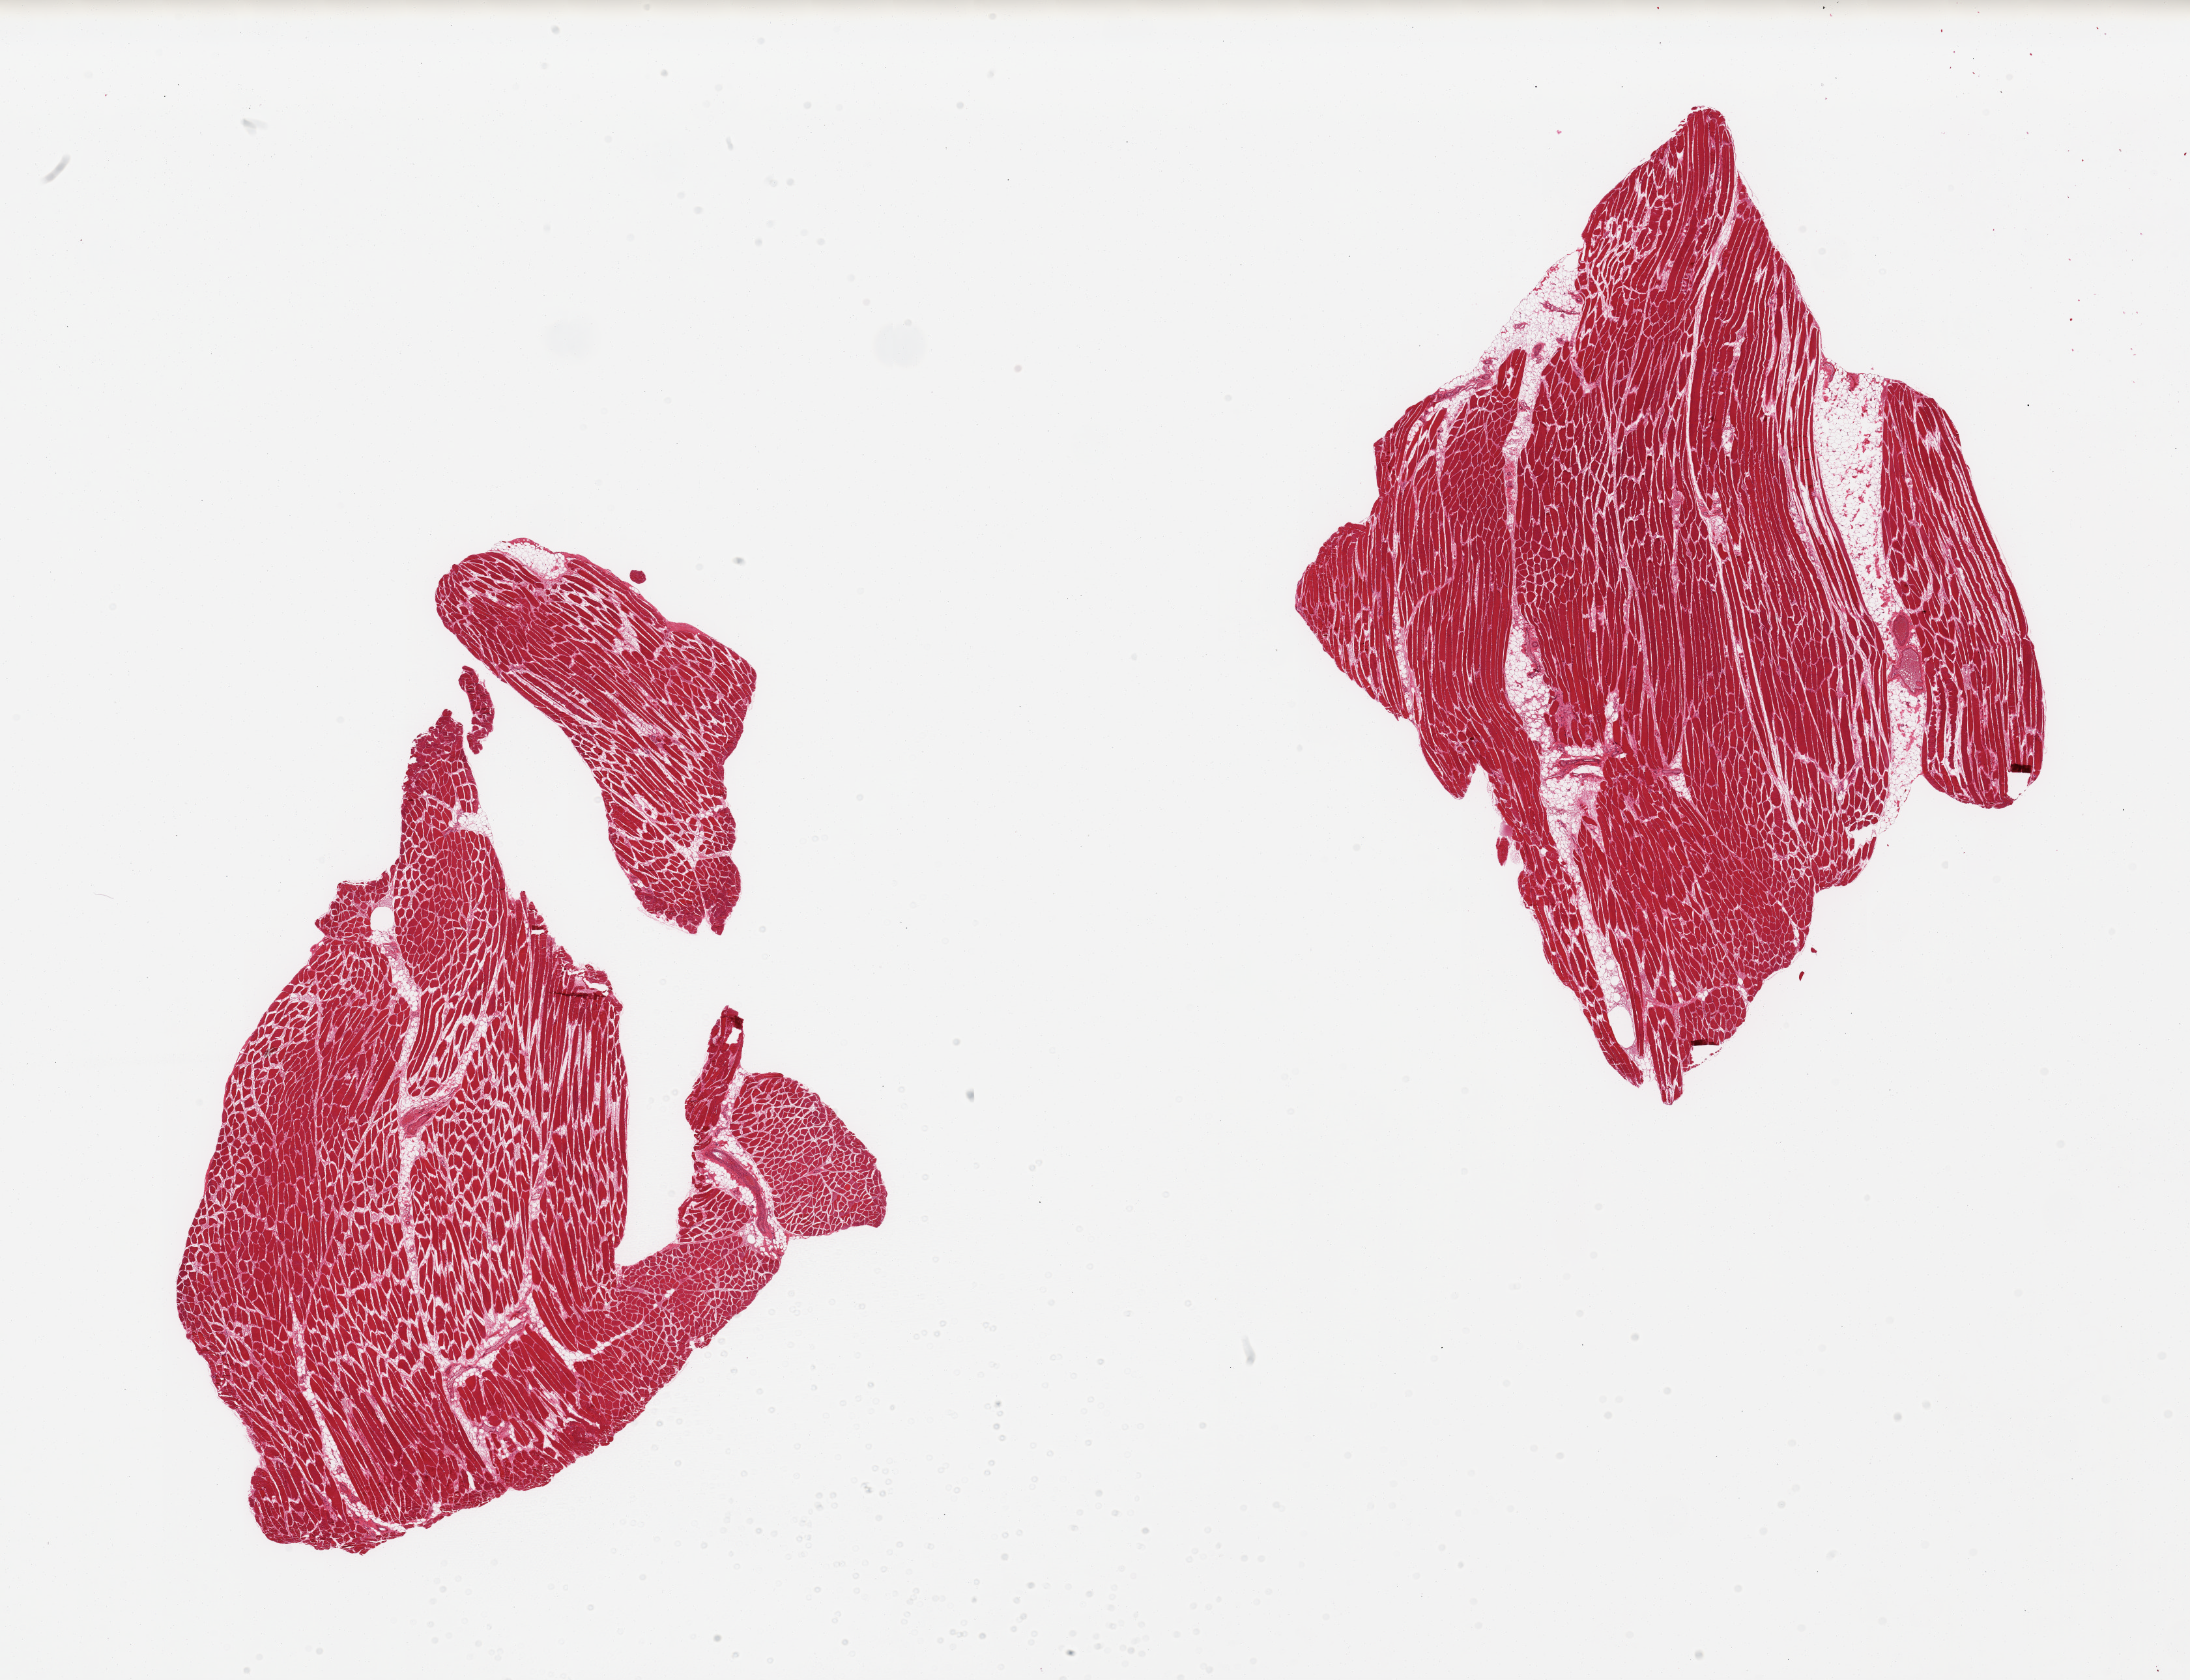
Digitized H&E-stained section — shown as a low-resolution overview of the whole scanned area (about 26.6 x 20.4 mm). PAXgene-fixed paraffin-embedded (PFPE) section. Section of skeletal muscle (target tissue). Tissue donor sample. Male donor.
* reviewer comment on this tissue sample: 2 pieces; 1 piece has 10% internal fat